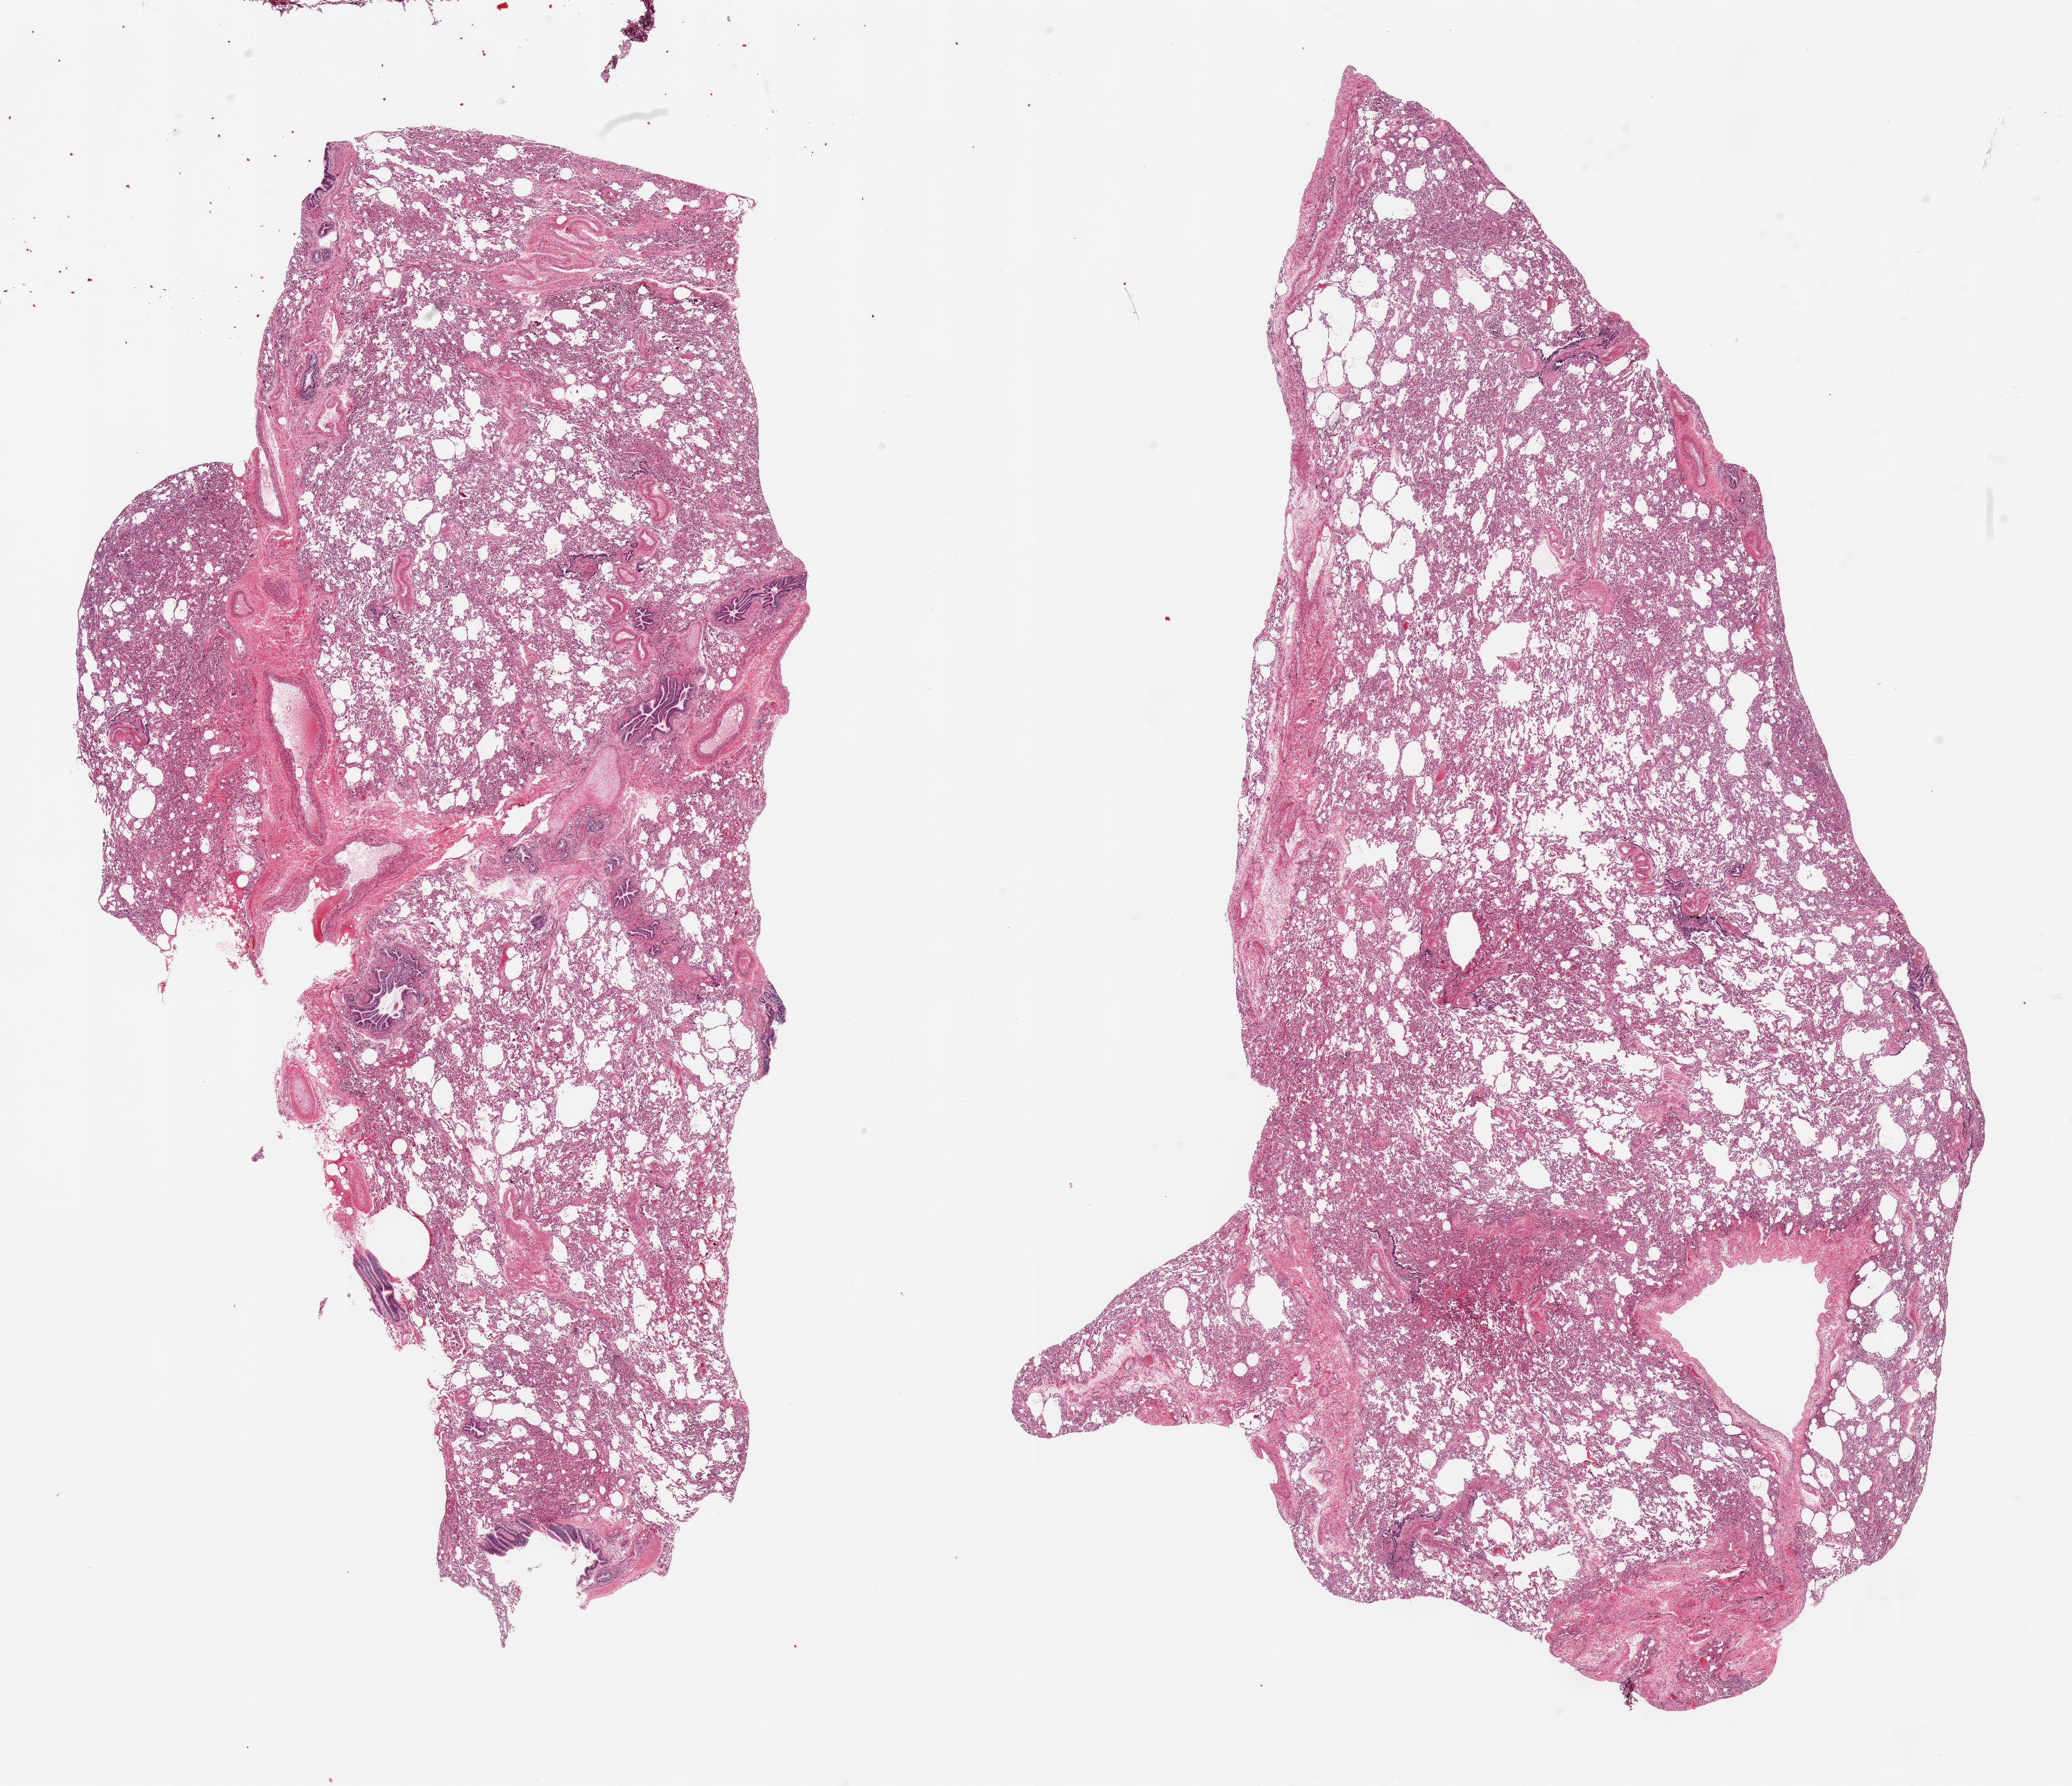
Digitized hematoxylin and eosin (H&E)-stained section, brightfield, a low-resolution overview of the entire scanned area, about 23.6 x 20.4 mm (from a 20x scan), PAXgene-fixed paraffin-embedded (PFPE) section, section of lung (target tissue), donor tissue sample. Male donor.
- review note (as recorded): 2 pieces, focal early pneumonitis, diffuse atalectasis, bronchial mucosa fairly prominent